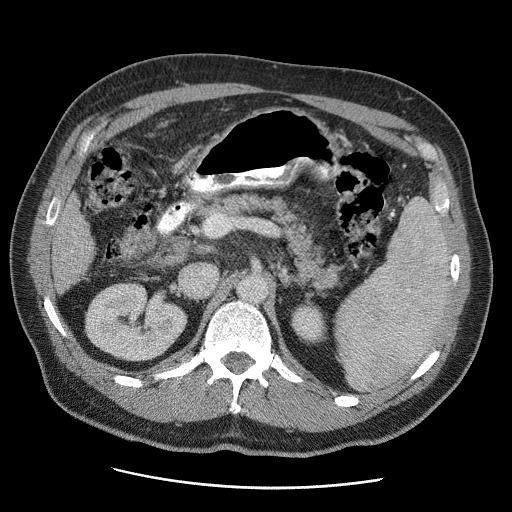
Contrast-enhanced abdominal CT (liver protocol), one axial slice; slice 15 of 81 in the series (ordered by position); reconstruction kernel STANDARD; 120 kVp; soft-tissue window (W 400 / L 40 HU); 512 × 512 image matrix, field of view 380 × 380 mm. Case-level facts recorded for this patient, not image findings: diagnosis: hepatocellular carcinoma (patient treated with transarterial chemoembolisation; whether this scan precedes or follows treatment is not stated here); TNM stage (as recorded): Stage-IIIA; Child-Pugh class: A; tumour differentiation: moderately differentiated; tumour nodularity: multinodular.
Structures marked on this image (semi-automatic segmentation, software-assisted and operator-edited):
- liver parenchyma outside the tumour (the mass and vessels are separate outlines, so this box may not span the whole liver): bounding box (x1, y1, x2, y2) in pixels: (52, 193, 94, 292)